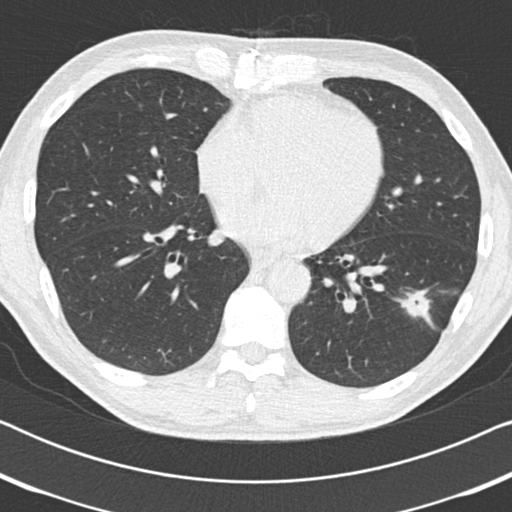
Low-dose screening chest CT, one axial slice. Slice 78 of 186 in the series (ordered by position). Reconstruction kernel B30f. Lung window (W 1500 / L -600 HU). 512 × 512 image matrix, field of view 330 × 330 mm.
Structures marked on this image (expert manual segmentation):
- lesion 1 (tumor, lower lobe of left lung): bounding box <402,292,432,319> (left, top, right, bottom; pixels)